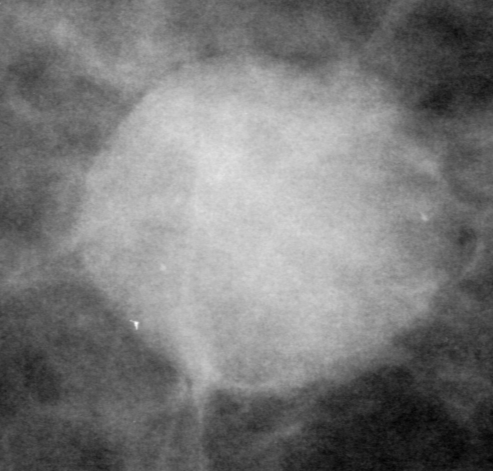
Region of interest cut from a scanned film mammogram (one marked finding); right breast; CC view.
- Marked abnormality: mass, shape round, margins spiculated; BI-RADS assessment category 3; pathology (as recorded): malignant.